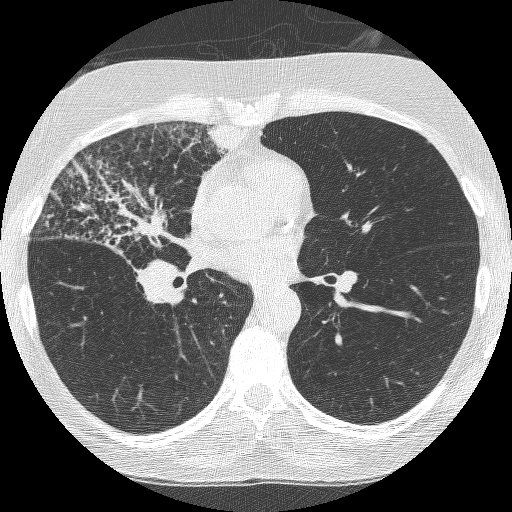
Chest CT (low-dose screening protocol), one axial image; third screening round (two years after baseline); lung window (W 1500 / L -600 HU); 1.25 mm slice thickness; lung (sharp) reconstruction kernel (BONE); slice 135 of 253 in the series; 512 × 512 image matrix, field of view 294 × 294 mm. Female, age 64 years at enrolment. Former smoker at enrolment.
Expert reader's lesion annotation, bounding box [x1, y1, x2, y2] px = [58, 165, 200, 310]. Reader record for this screening exam (exam-level; its link to the box is not recorded): non-calcified nodule or mass ≥4 mm, right upper lobe, 49 × 43 mm, spiculated (stellate) margins, soft tissue attenuation, pre-existing on the prior screen: yes; interval growth: yes. Official screen result: positive, other. Lung cancer was diagnosed 7 days after this screen: adenocarcinoma, NOS, right upper lobe, right middle lobe, right hilum, stage IV (AJCC 6th edition), 85 mm at pathology.